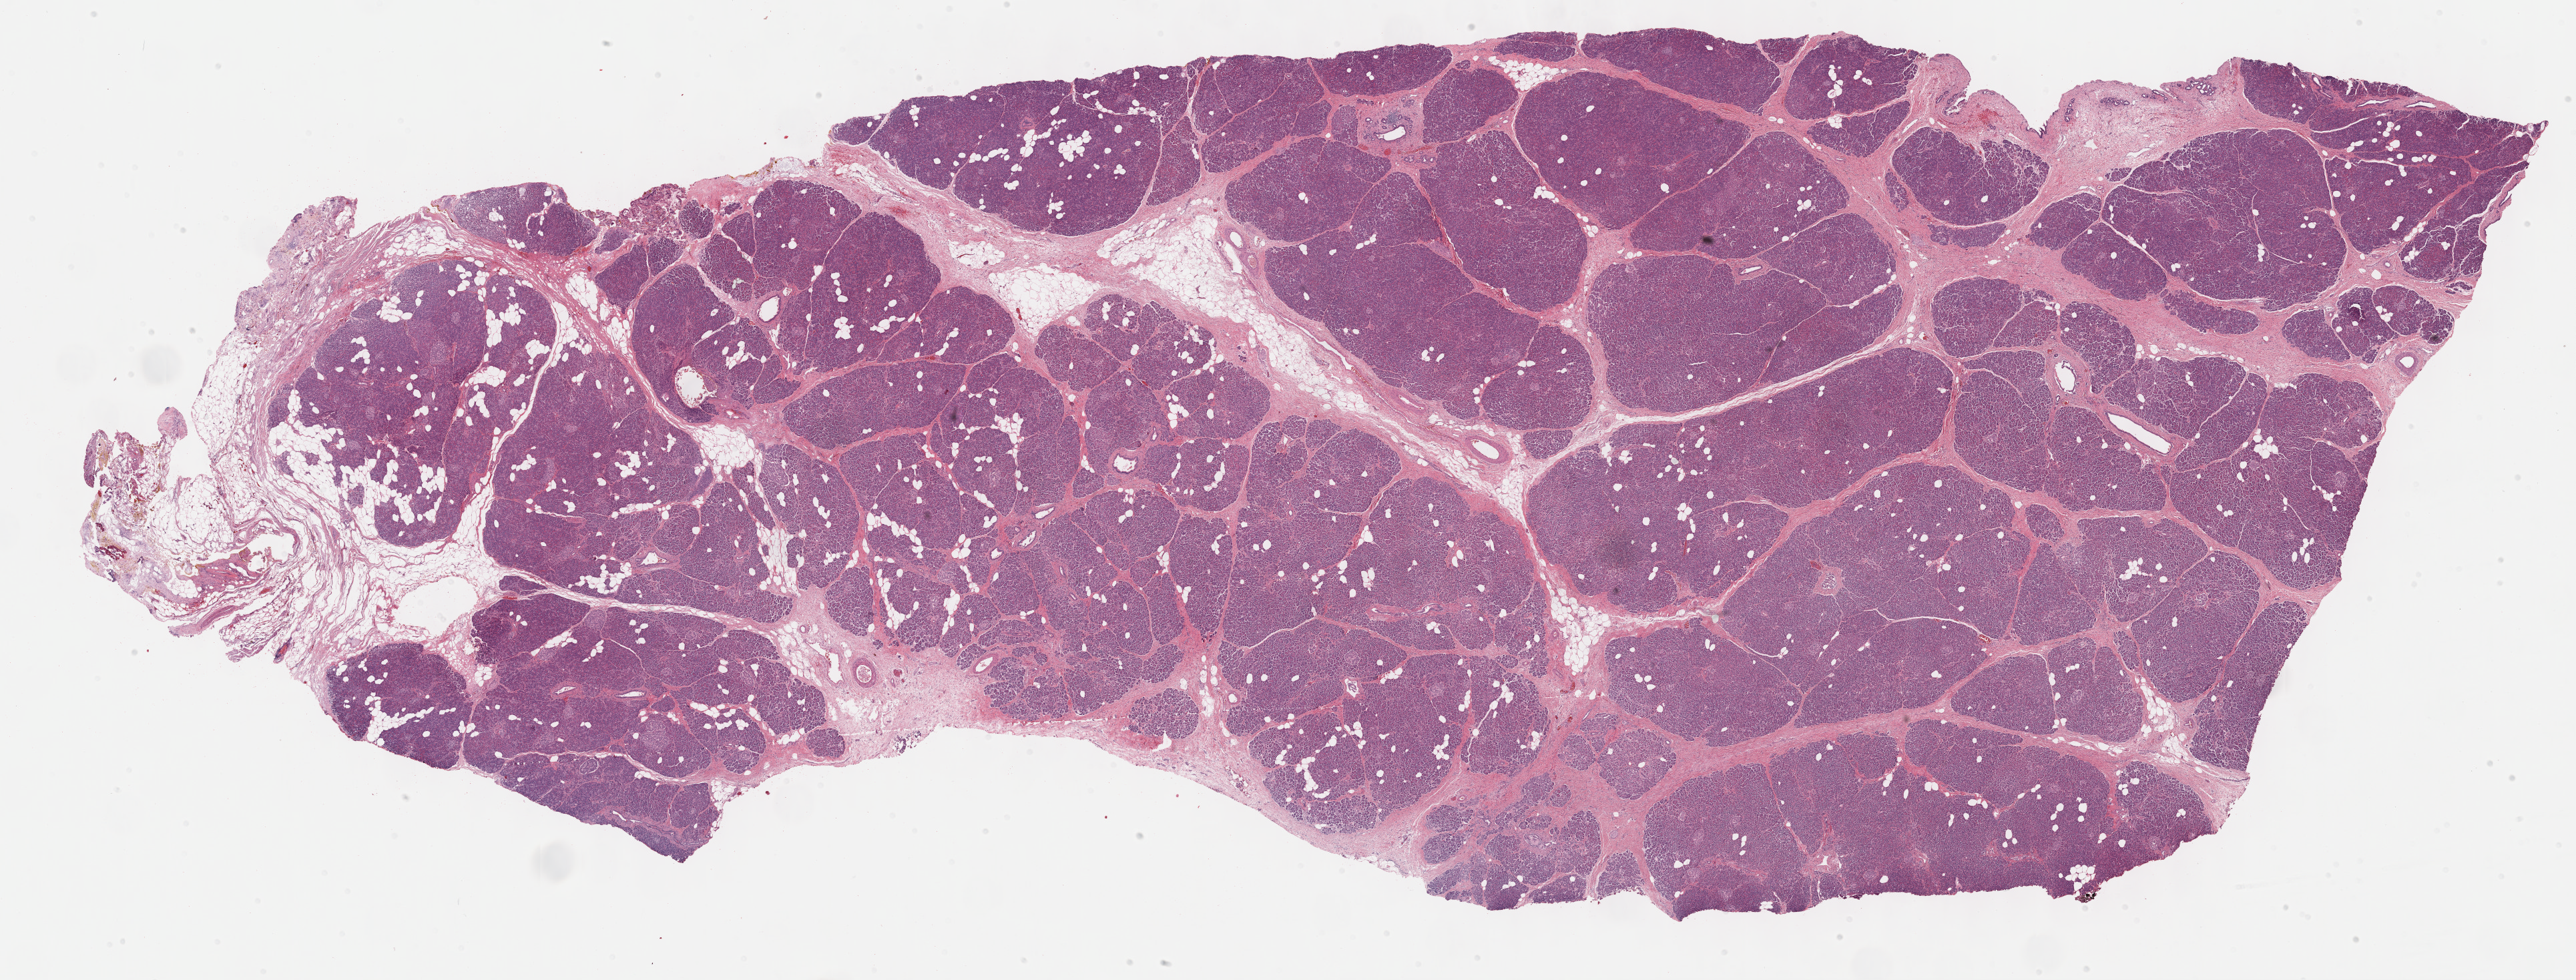
H&E-stained whole-slide image — a low-resolution overview of the entire scanned area, about 31.2 x 11.9 mm (from a 40x scan), FFPE section, sample: primary tumour, pancreas. Male patient; age at initial diagnosis 71 years. Histologic grade: G1 (well differentiated).
* AJCC pathologic stage: IV (6th edition)
* lymph nodes positive (case pathology): 1 of 13 examined
* histologic diagnosis: Infiltrating duct carcinoma, NOS (head of pancreas)